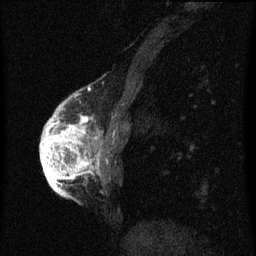
Breast MRI (dynamic contrast-enhanced), one sagittal slice. Position 18 of 60 along the scan axis. Dynamic contrast-enhanced series, image 2 of 3 at this slice position (ordered by acquisition). 1.5 T. TE 4.2 ms, TR 8 ms. 256 × 256 image matrix, field of view 180 × 180 mm. Patient: female, 56 years.
Annotated regions visible in this slice (semi-automatically segmented with operator editing):
- analysis volume of interest (the breast-tissue region the enhancement analysis was run in; not a lesion): bounding box [x1, y1, x2, y2] px = [42, 110, 101, 193]
- tumour enhancement mask (voxels above the 70 % enhancement threshold inside the analysis volume of interest): [42, 116, 99, 193]